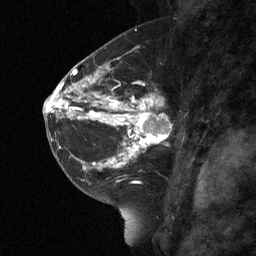
Breast MRI (dynamic contrast-enhanced), one sagittal slice; slice 35 of 64 in the series (ordered by position); dynamic contrast-enhanced study with each time point stored as its own series, time point 2 of 3 at this slice position (early post-contrast, ordered by acquisition time); 1.5 T; TE 4.8 ms, TR 27 ms; 2 mm slice thickness; 256 × 256 image matrix, field of view 180 × 180 mm. Patient: female, 42 years. Case-level facts recorded for this patient, not image findings: setting: breast cancer imaged before/during neoadjuvant chemotherapy; receptor status: triple-negative.
Outlined on this slice (semi-automatic segmentation, software-assisted and operator-edited):
- analysis volume of interest (the breast-tissue region the enhancement analysis was run in; not a lesion): bounding box <115,85,181,160> (left, top, right, bottom; pixels)
- tumour enhancement mask (voxels above the 90 % enhancement threshold inside the analysis volume of interest): <115,98,163,160>